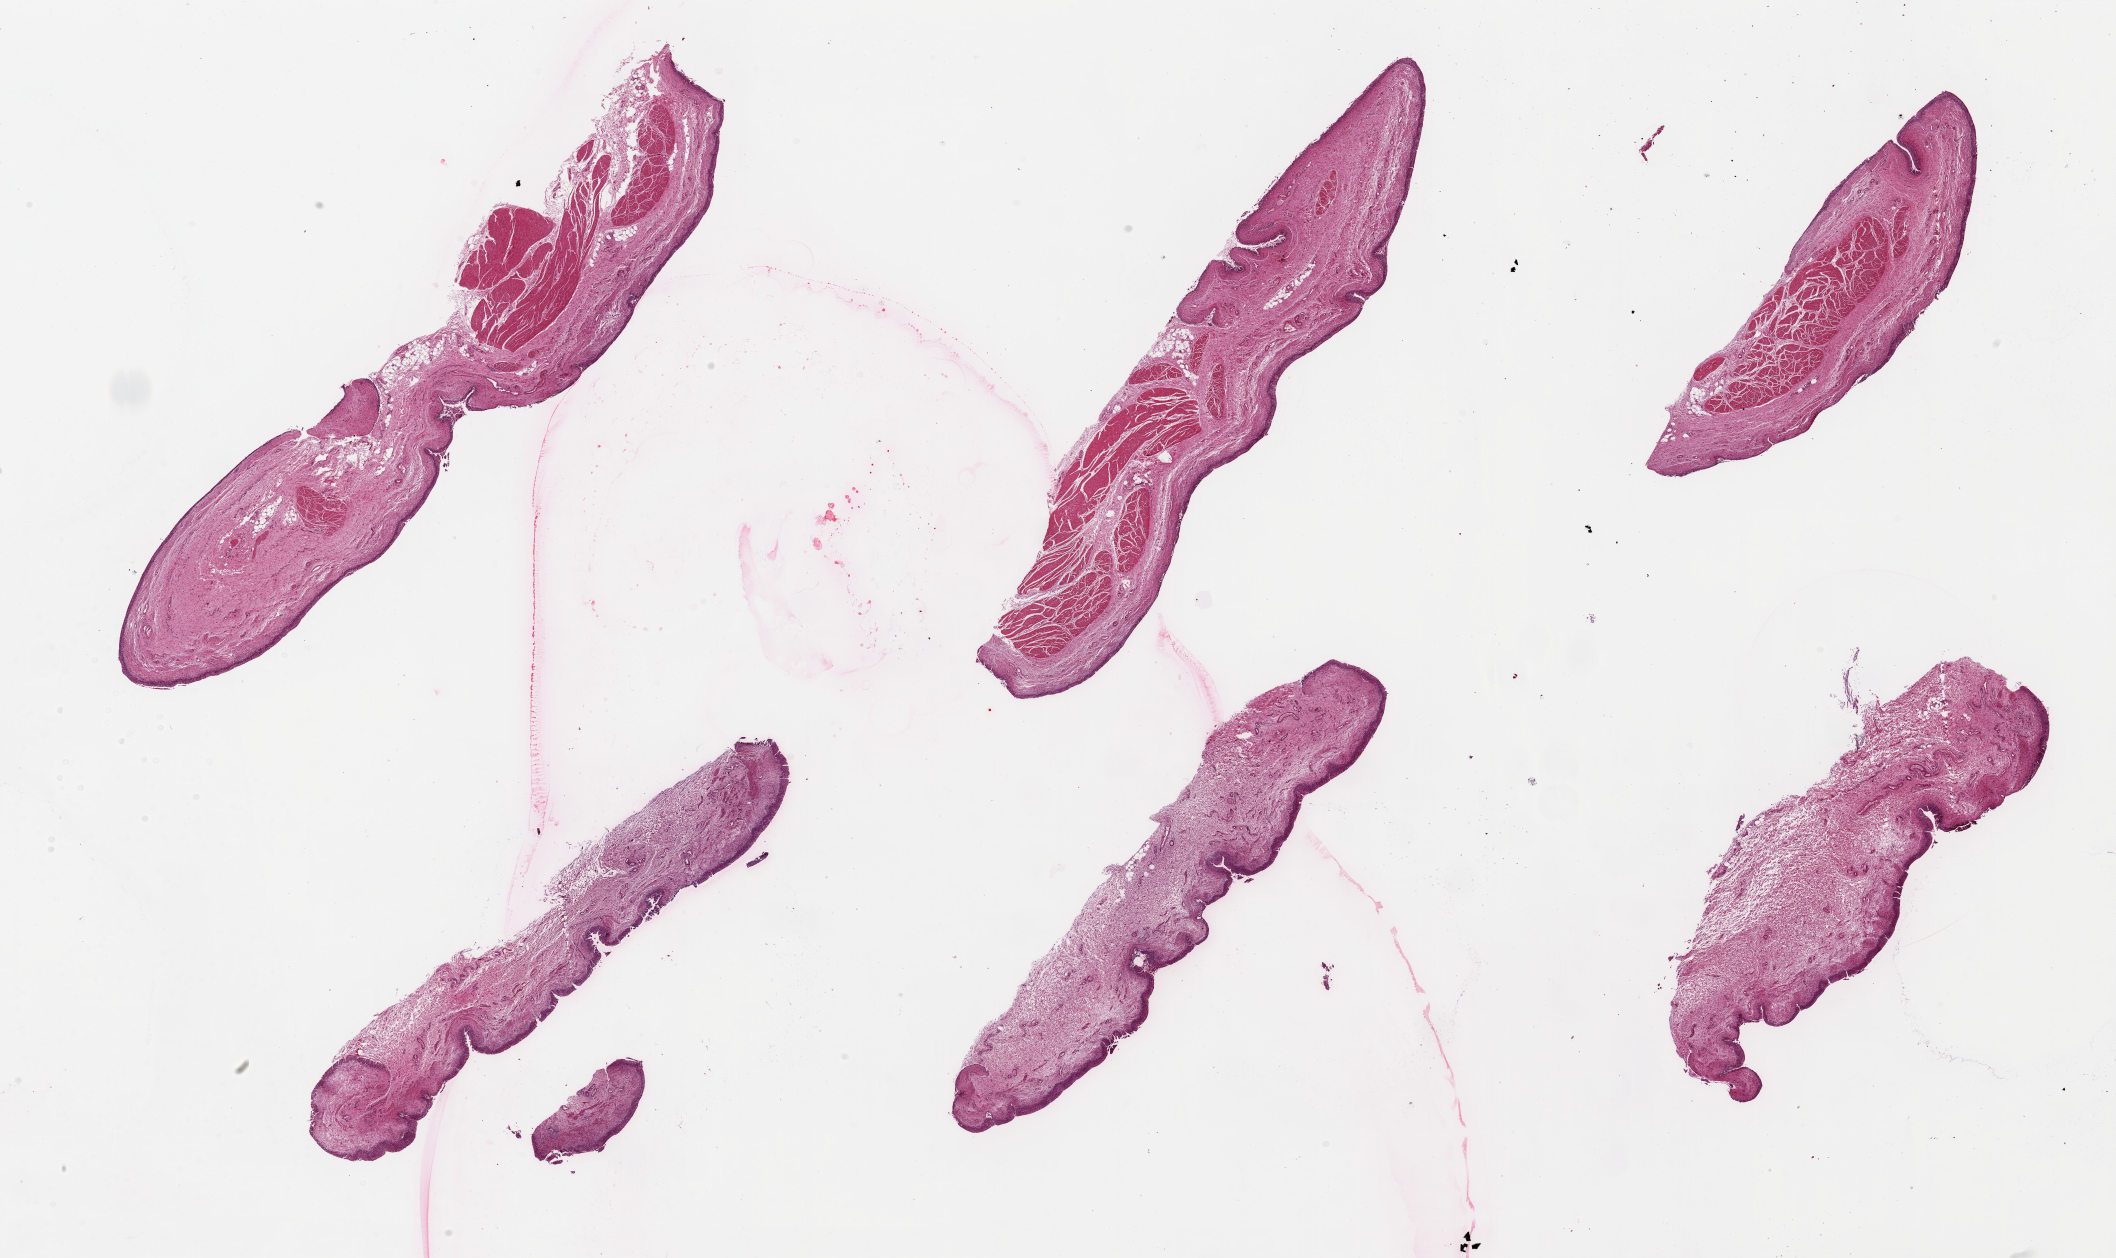
Whole-slide image, hematoxylin and eosin (H&E) stain, low-resolution overview of the scanned area, about 33.5 x 19.9 mm (from a 20x scan); PAXgene-fixed paraffin-embedded (PFPE) section; section of vagina (target tissue); tissue donor sample. Donor sex: female.
• reviewer comment on this tissue sample: 6 pieces, up to 13x3mm; glandular metaplasia noted